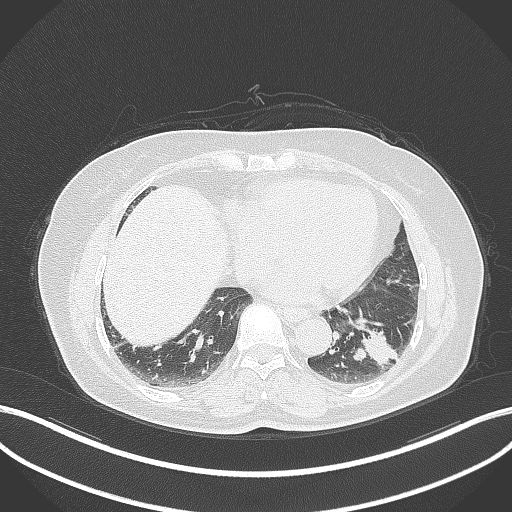
Chest CT, one axial slice. Slice 126 of 311 in the series (ordered by position). 120 kVp. Lung window (W 1500 / L -600 HU). 1 mm slice thickness. 512 × 512 image matrix. Female patient, age 59 years. Case-level facts recorded for this patient, not image findings: clinical TNM (as recorded): T2a N0 M0; histopathological grade: G2-3.
Outlined on this slice (bounding box drawn by a radiologist):
- lung tumour (recorded histology: adenocarcinoma): box from (x=350, y=325) to (x=399, y=371) px